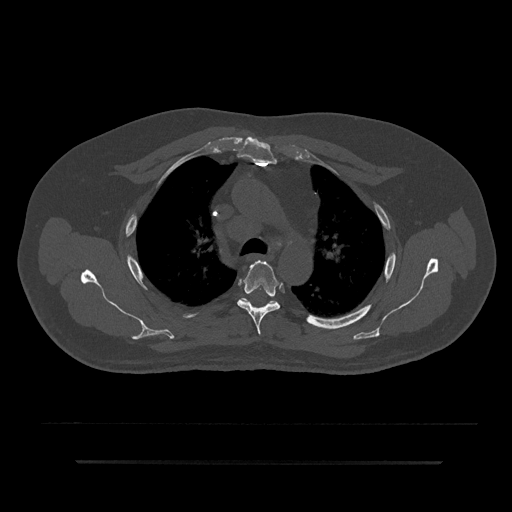
CT including the spine, one axial slice; slice 612 of 797 in the series (ordered by position); reconstruction kernel Br40s/3; 120 kVp; bone window (W 1800 / L 400 HU); 0.5 mm slice thickness; 512 × 512 image matrix, field of view 464 × 464 mm. Male patient, age 59 years. From the clinical record (not read from this slice): primary cancer: bile ducts; vertebrae with lytic lesions (as recorded): T10.
Outlined on this slice (semi-automatic segmentation, software-assisted and operator-edited):
- T4 vertebra: box from (x=237, y=260) to (x=282, y=335) px
- T5 vertebra: (x=237, y=298)–(x=279, y=305)